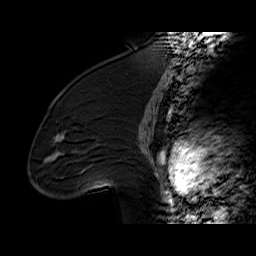
Breast MRI (dynamic contrast-enhanced), one sagittal slice; position 39 of 60 along the scan axis; dynamic contrast-enhanced series, time point 2 of 6 at this slice position (early post-contrast); 1.5 T; TE 6.2 ms, TR 32.4 ms; 256 × 256 image matrix, field of view 200 × 200 mm. Female patient. From the clinical record (not read from this slice): setting: breast cancer imaged before/during neoadjuvant chemotherapy; receptor status: triple-negative.
Annotated regions visible in this slice (semi-automatically segmented with operator editing):
- analysis volume of interest (the breast-tissue region the enhancement analysis was run in; not a lesion): box from (x=36, y=97) to (x=134, y=196) px
- tumour enhancement mask (voxels above the 100 % enhancement threshold inside the analysis volume of interest): (x=55, y=136)–(x=102, y=183)